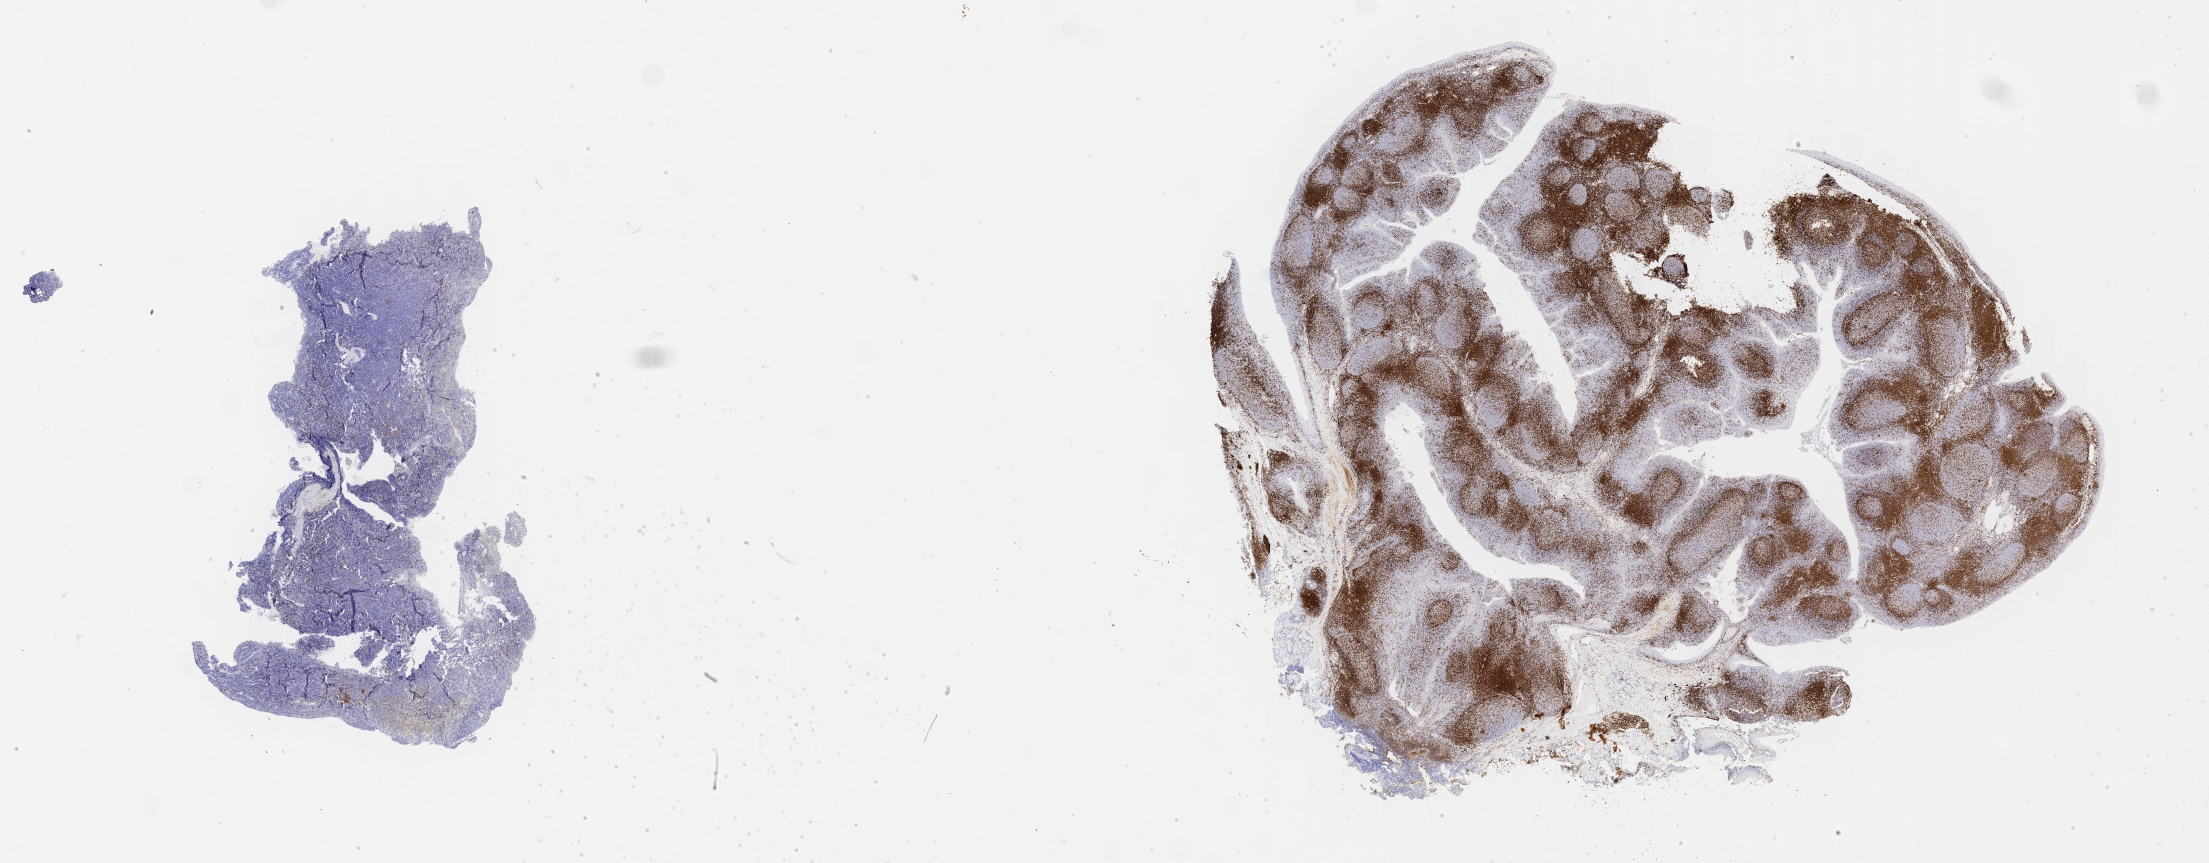
IHC for CD3, whole-slide image, low-resolution overview of the scanned area, about 35.7 x 14.0 mm; tumor tissue; anatomic site: cranium. Patient: female, 10 years old.
• histologic diagnosis: Burkitt lymphoma, NOS